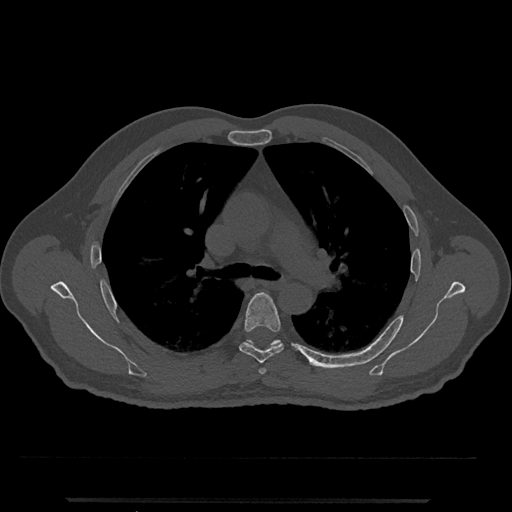
CT including the spine, one axial slice; position 785 of 797 along the scan axis; 120 kVp; bone window (W 1800 / L 400 HU); 0.5 mm slice thickness; 512 × 512 image matrix, field of view 419 × 419 mm. Male patient, age 63 years. From the clinical record (not read from this slice): primary cancer: prostate.
Outlined on this slice (semi-automatically segmented with operator editing):
- T5 vertebra: bounding box <239,292,284,364> (left, top, right, bottom; pixels)
- T6 vertebra: <245,339,281,347>